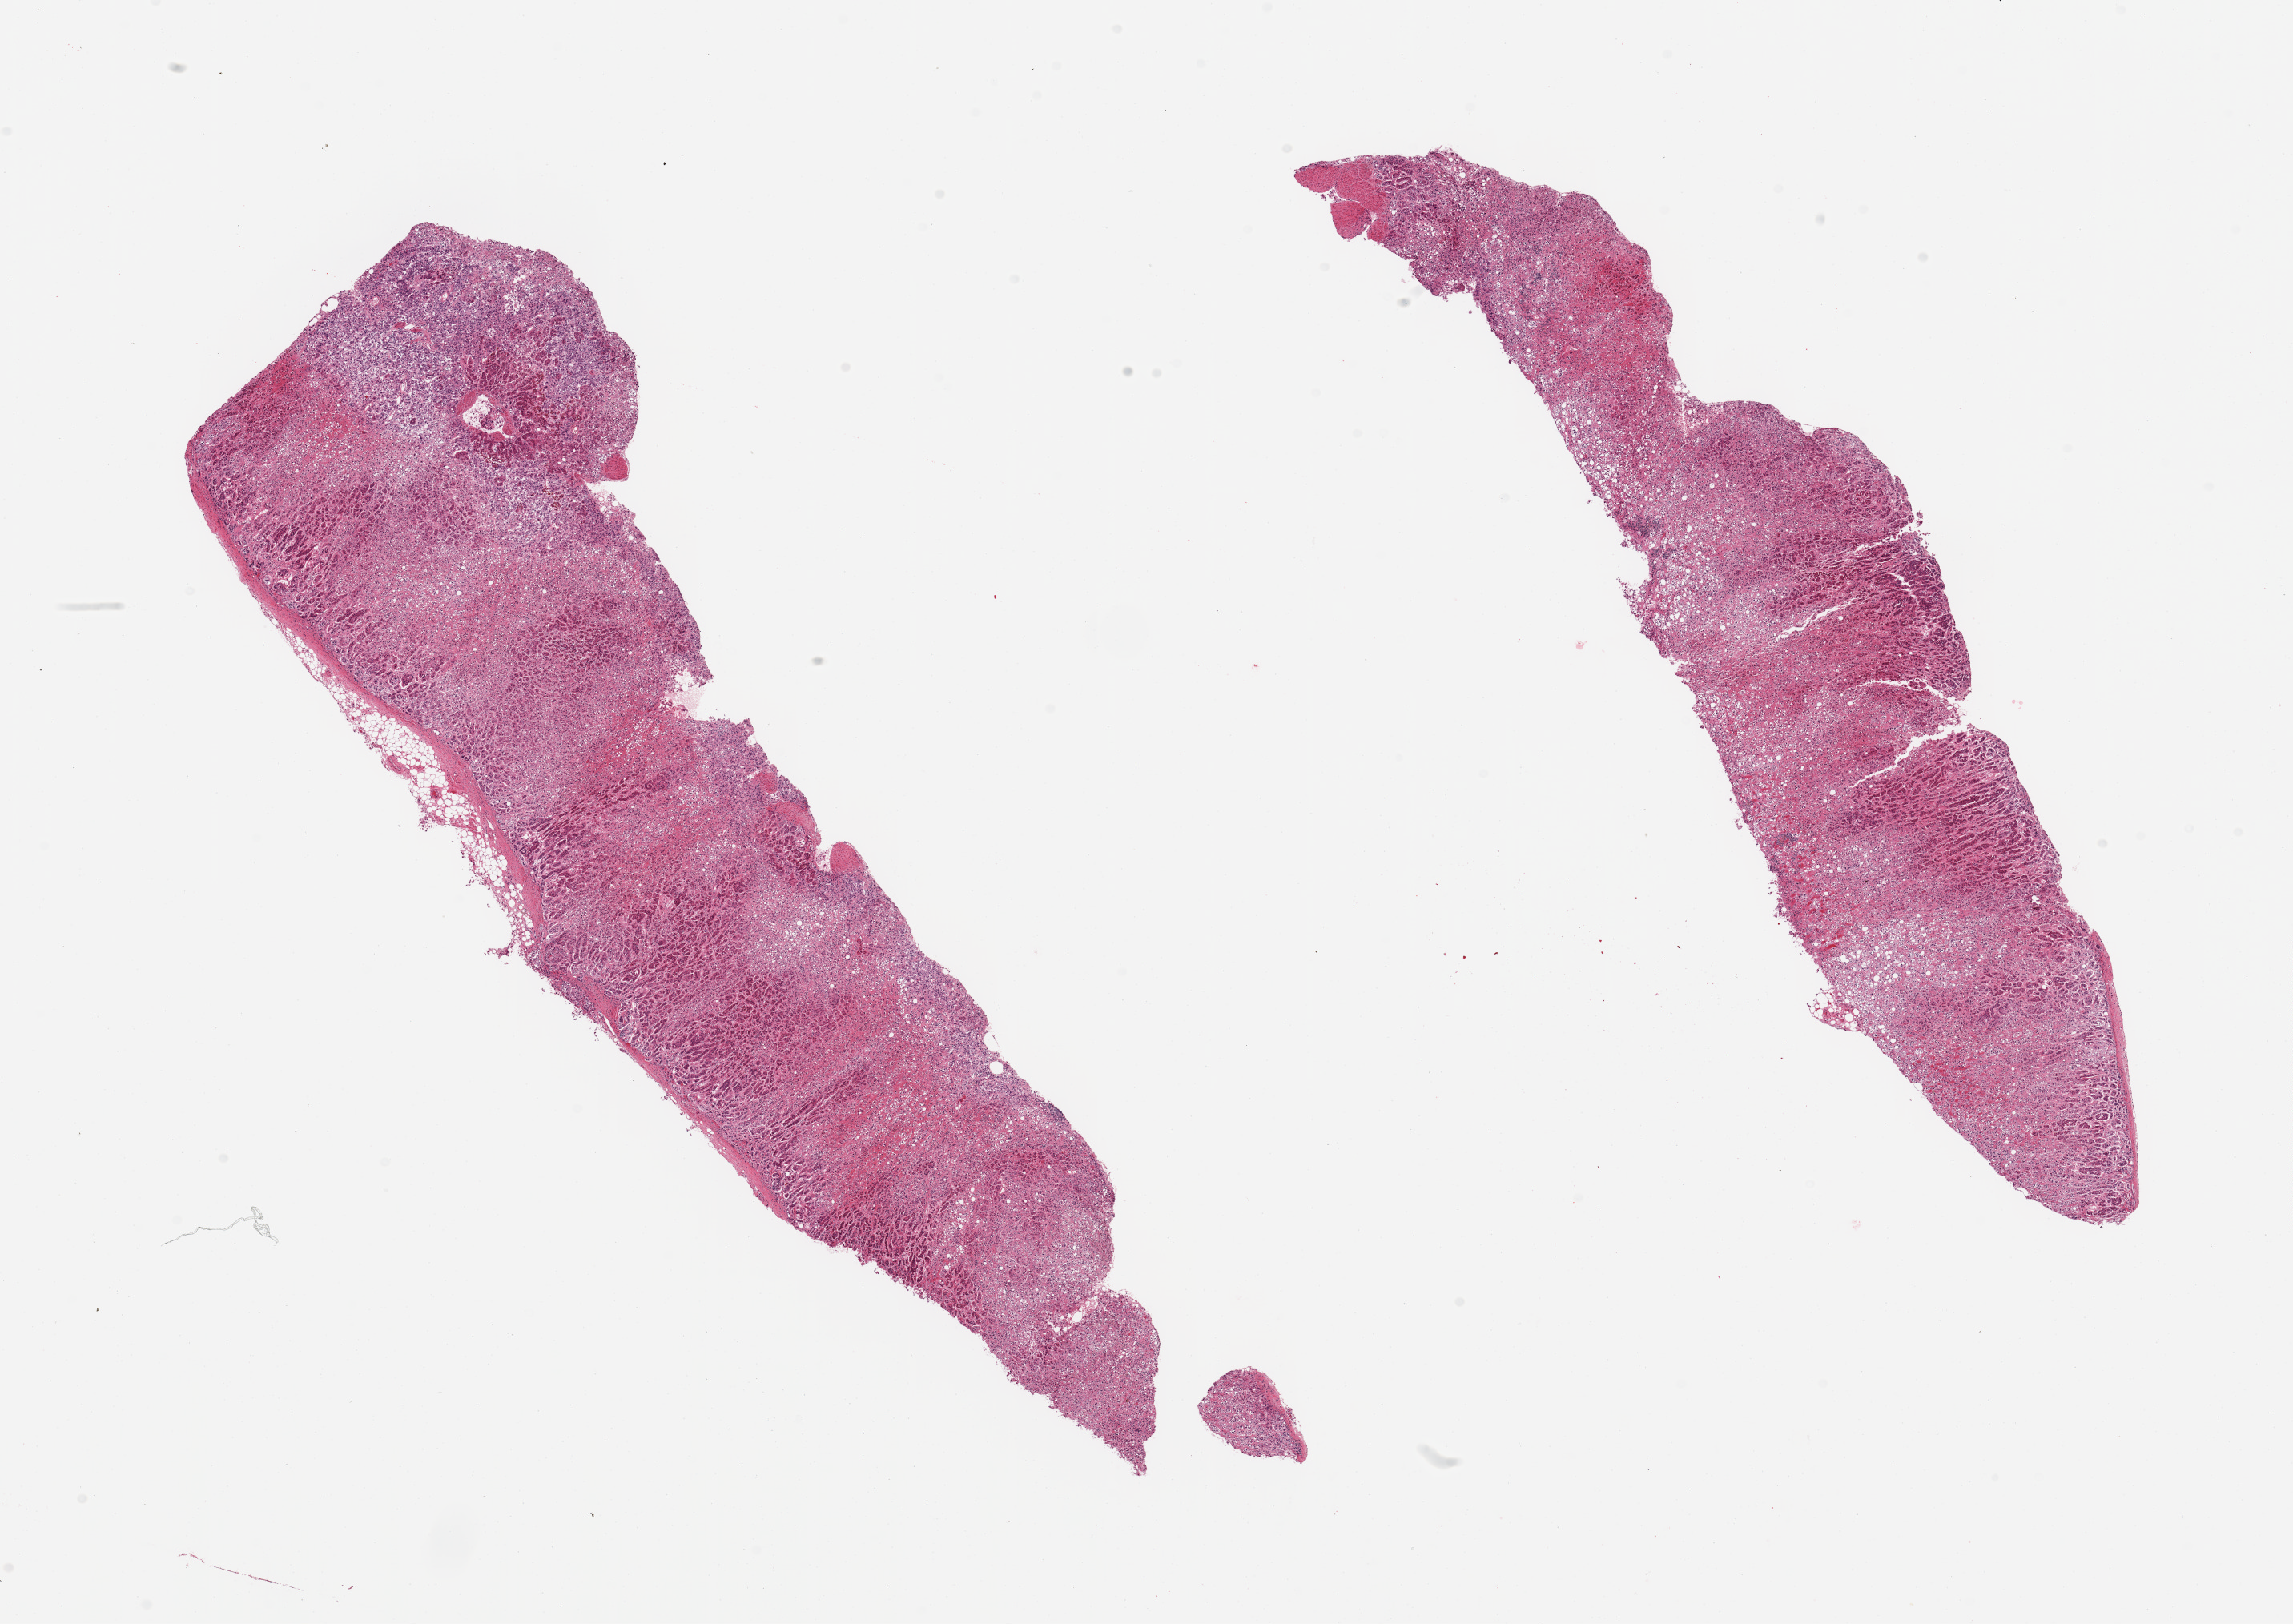
Digitized hematoxylin and eosin (H&E)-stained section, brightfield — whole scanned area (about 22.6 x 16.0 mm, from a 20x scan) shown as a low-resolution overview. PAXgene-fixed paraffin-embedded (PFPE) section. Target tissue: adrenal gland. Donor tissue sample. Donor sex: male.
• review note (as recorded): 2 pieces, cortex only